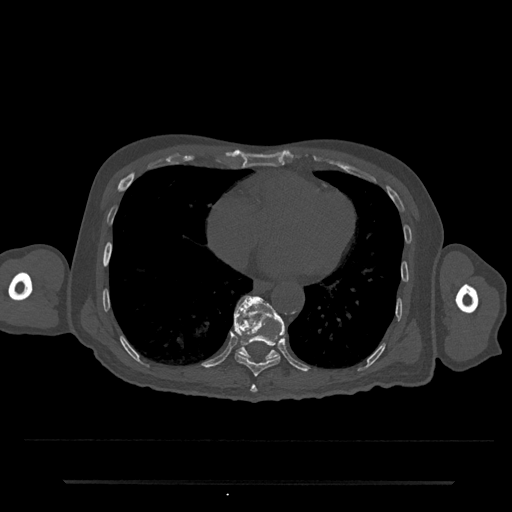
CT including the spine, one axial slice; slice 349 of 797 in the series (ordered by position); 120 kVp; bone window (W 1800 / L 400 HU); 0.5 mm slice thickness; 512 × 512 image matrix. Male patient, age 74 years. From the clinical record (not read from this slice): primary cancer: prostate.
Structures marked on this image (semi-automatic segmentation, software-assisted and operator-edited):
- T10 vertebra: box from (x=234, y=296) to (x=285, y=360) px
- T8 vertebra: (x=250, y=385)–(x=258, y=393)
- T9 vertebra: (x=234, y=296)–(x=285, y=377)